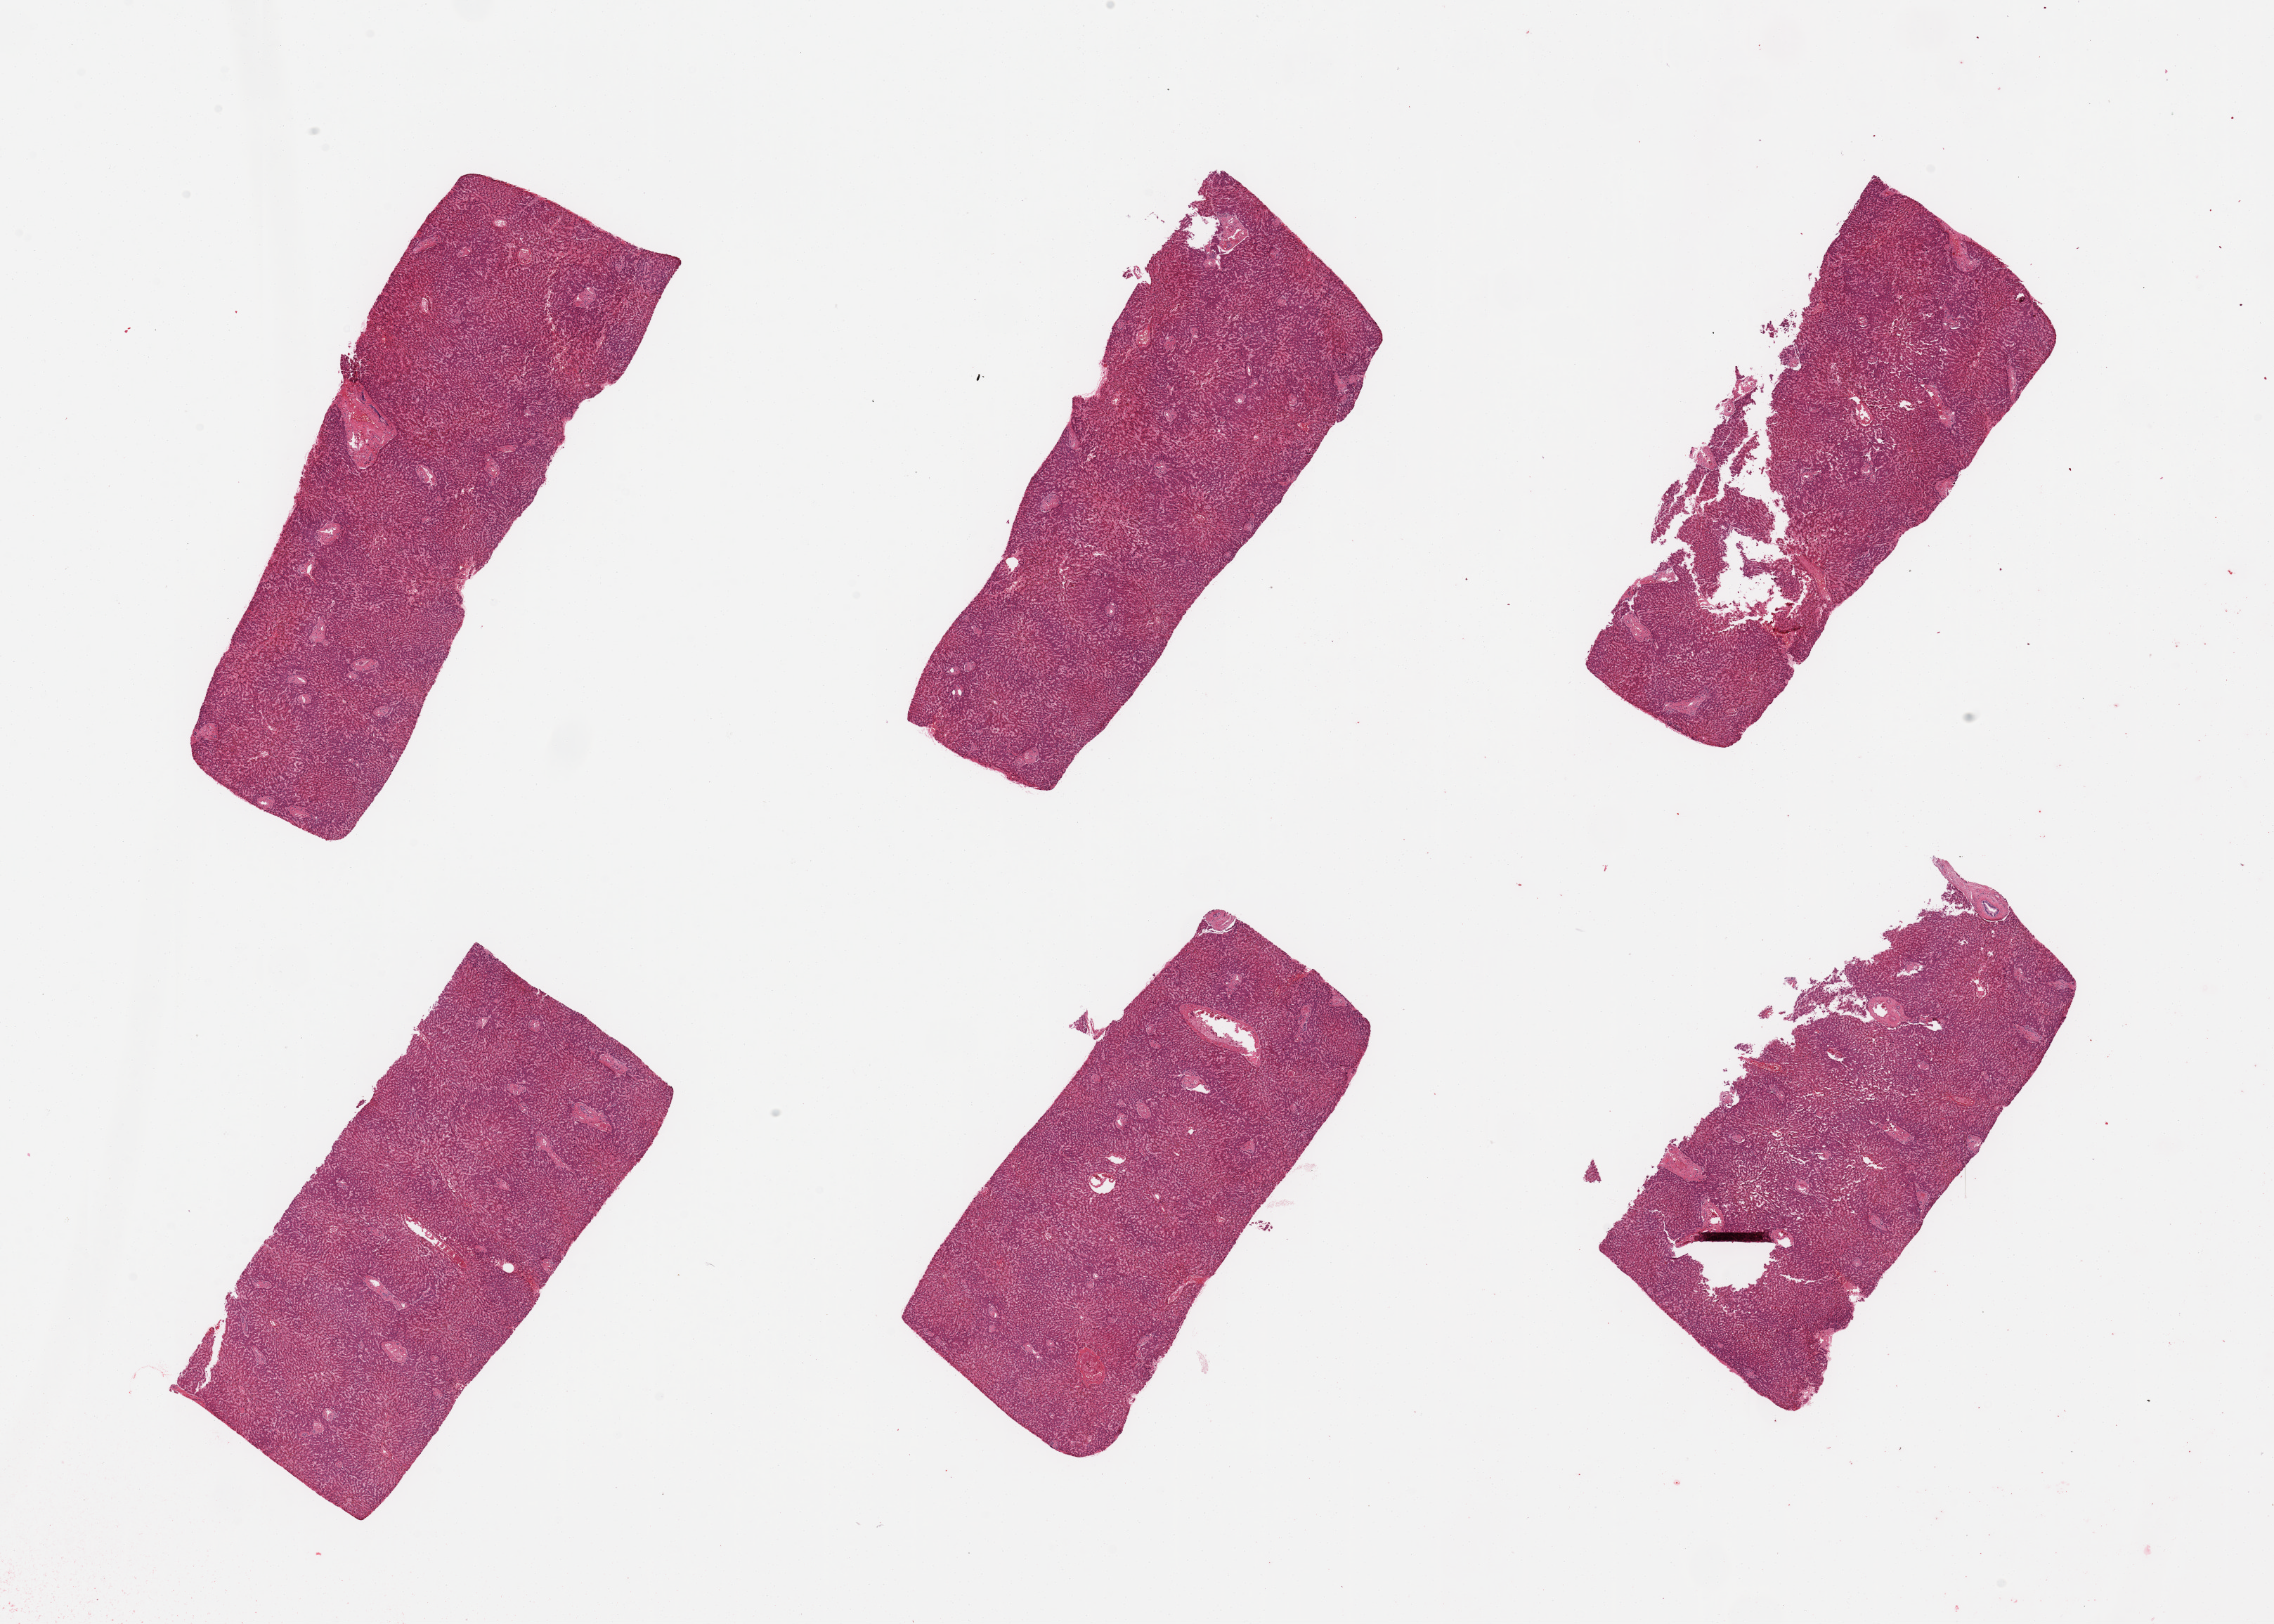
Digitized haematoxylin and eosin-stained section — shown as a low-resolution overview of the whole scanned area (about 25.6 x 18.3 mm, acquisition: 20x scan); PAXgene-fixed, paraffin-embedded tissue; target tissue: liver; tissue donor sample. Male donor.
• reviewer comment on this tissue sample: 1 pieces; liver, not skin